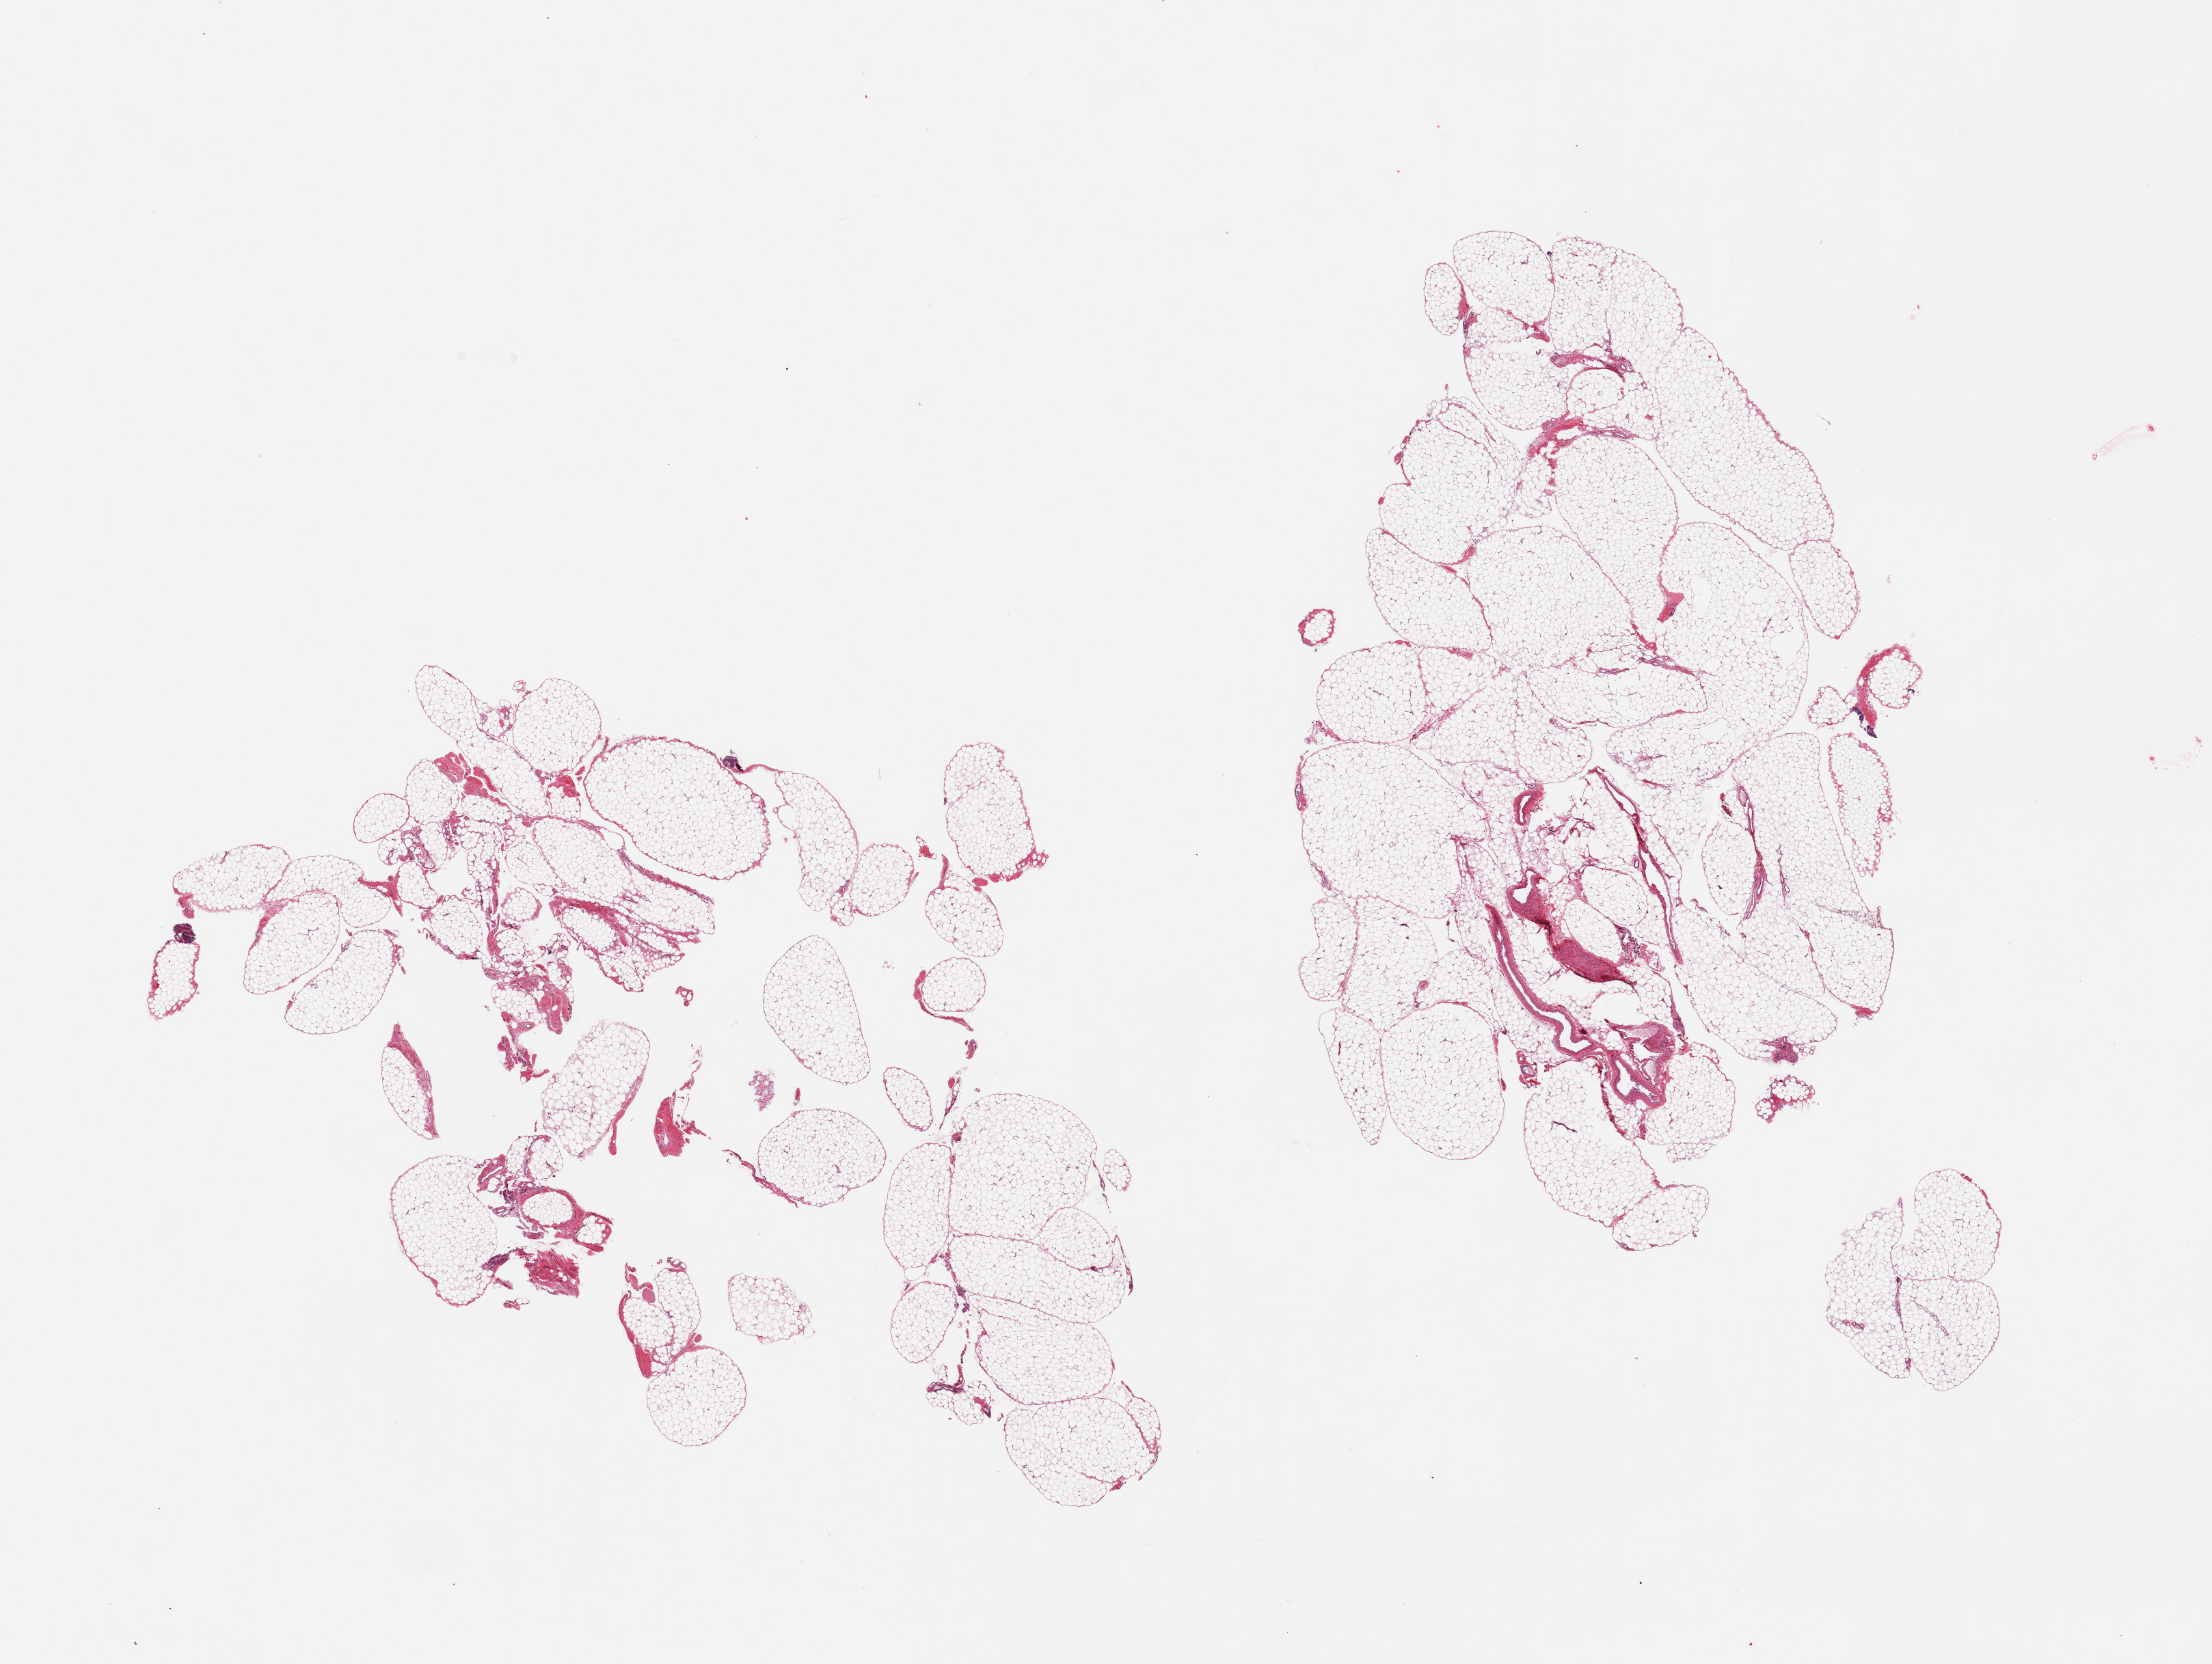
Digitized H&E-stained section, brightfield, low-resolution overview of the scanned area, about 25.6 x 19.3 mm, PAXgene-fixed paraffin-embedded (PFPE) section, target tissue: omentum, tissue donor sample. Donor sex: female.
- review note (as recorded): 2 pieces, minimal fibrovascular component